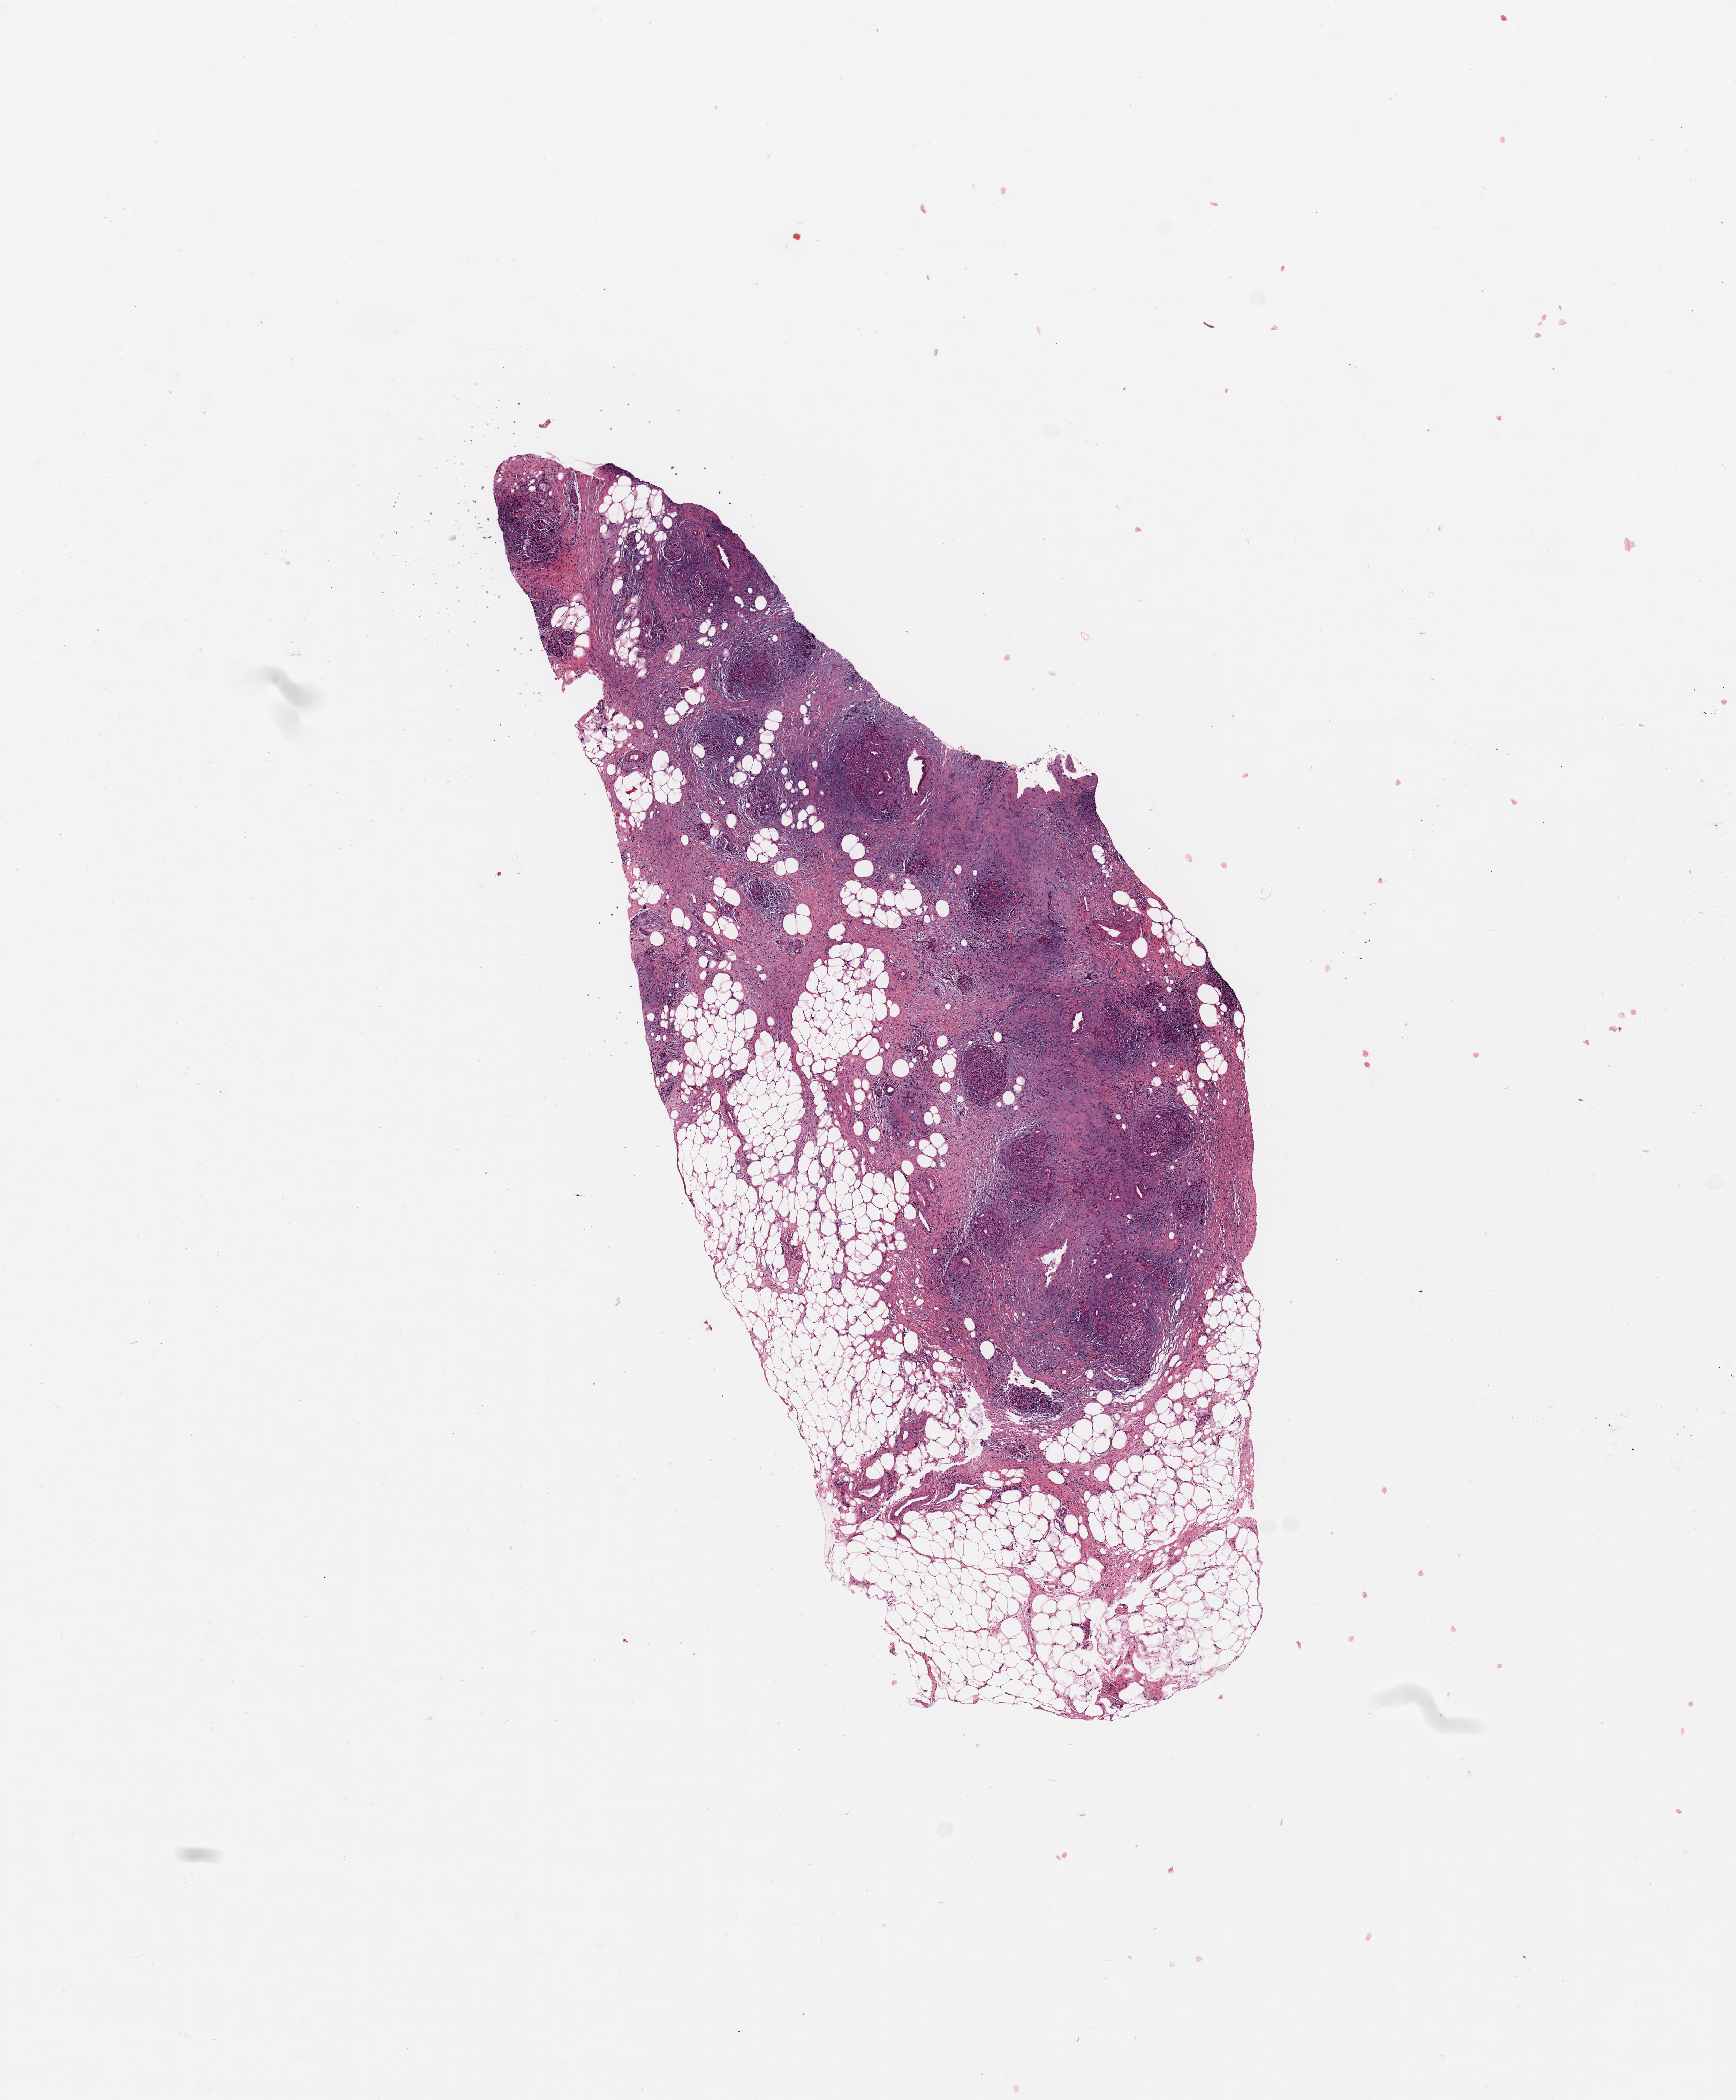
H&E whole-slide image — a low-resolution overview of the entire scanned area, about 9.8 x 11.9 mm (from a 20x scan). Pancreas, tissue type not recorded.
Patient diagnosis (cohort enrolment): ductal adenocarcinoma (pancreas).